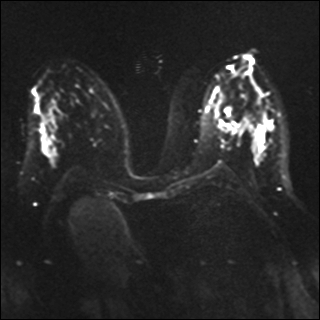
Breast MRI, one axial slice. Slice 18 of 41 in the series (ordered by position). Diffusion-weighted series; image 2 of 4 stored at this slice position (different b-values; order by instance number). 1.5 T. 4 mm slice thickness. 320 × 320 image matrix, field of view 340 × 340 mm. Female patient.
Structures marked on this image (outlined manually by an expert reader):
- tumour on diffusion-weighted imaging: bounding box (x1, y1, x2, y2) in pixels: (224, 125, 238, 133)